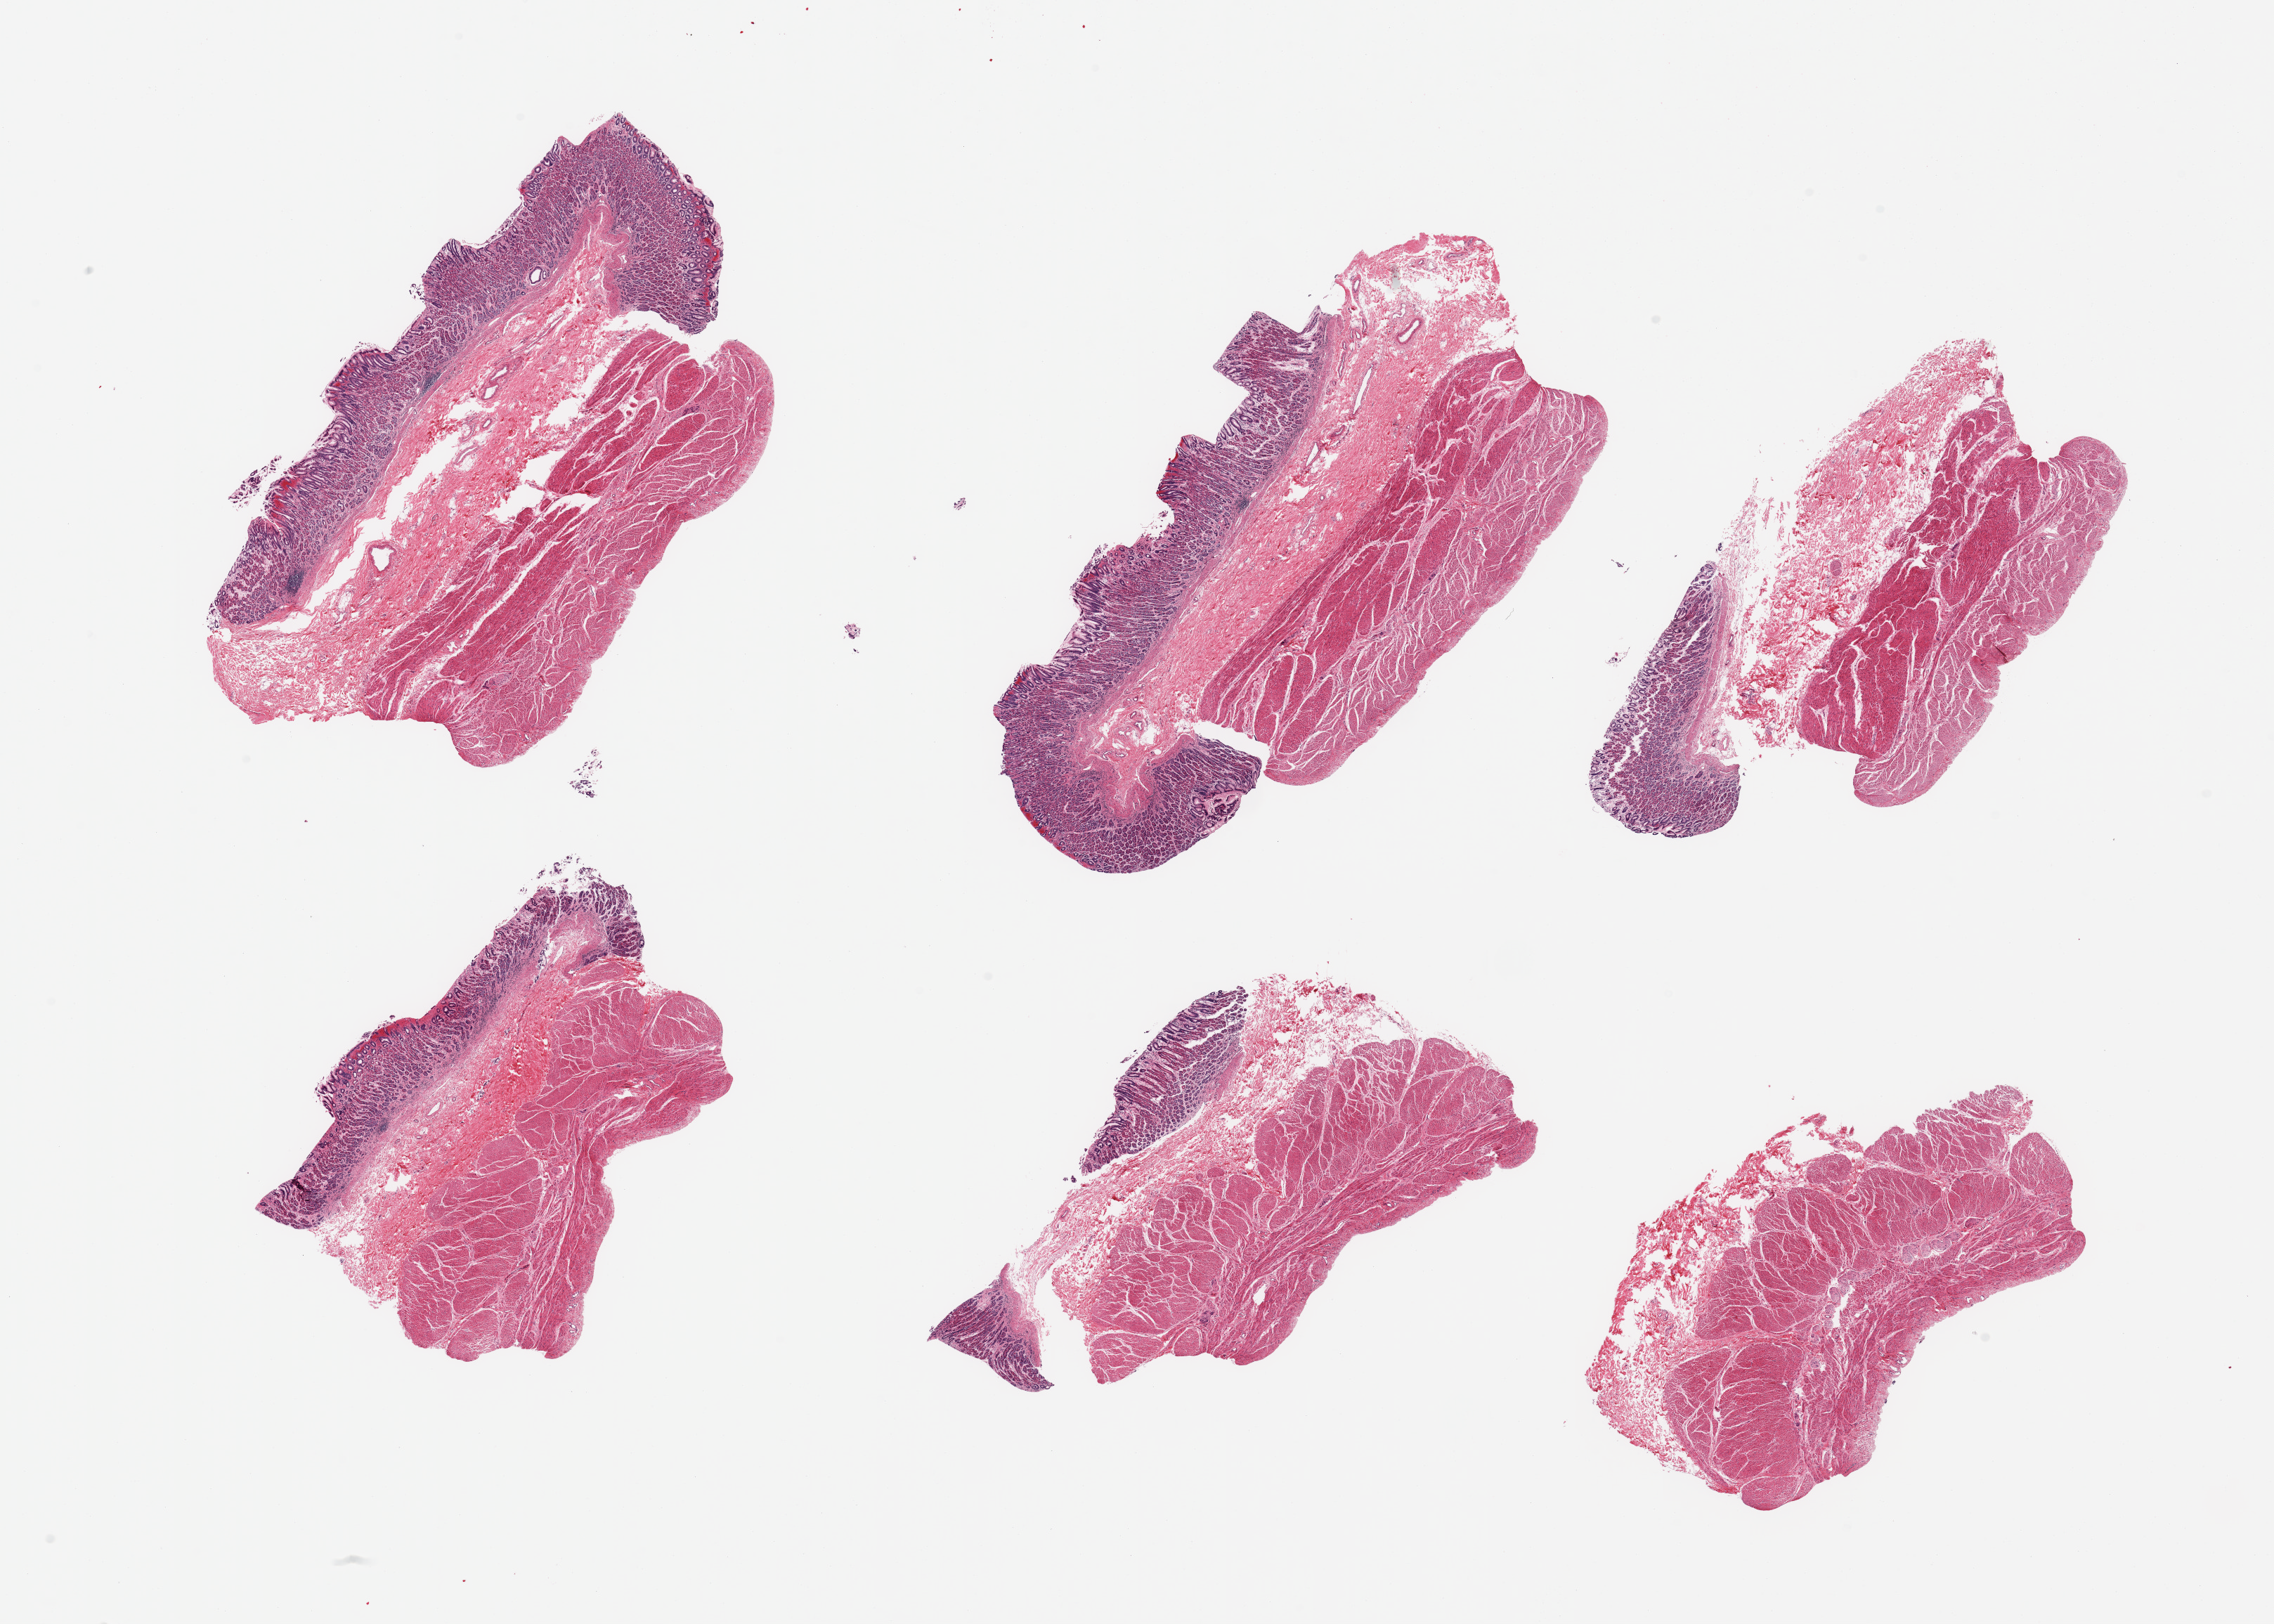
Haematoxylin and eosin whole-slide image, low-resolution overview of the scanned area, about 25.6 x 18.3 mm; PAXgene-fixed, paraffin-embedded tissue; sampled site (target tissue): stomach; tissue donor sample. Male donor.
• review note (as recorded): 6 pieces; one piece lacks surface mucosa; focal superficial mucosal fresh hemorrhage